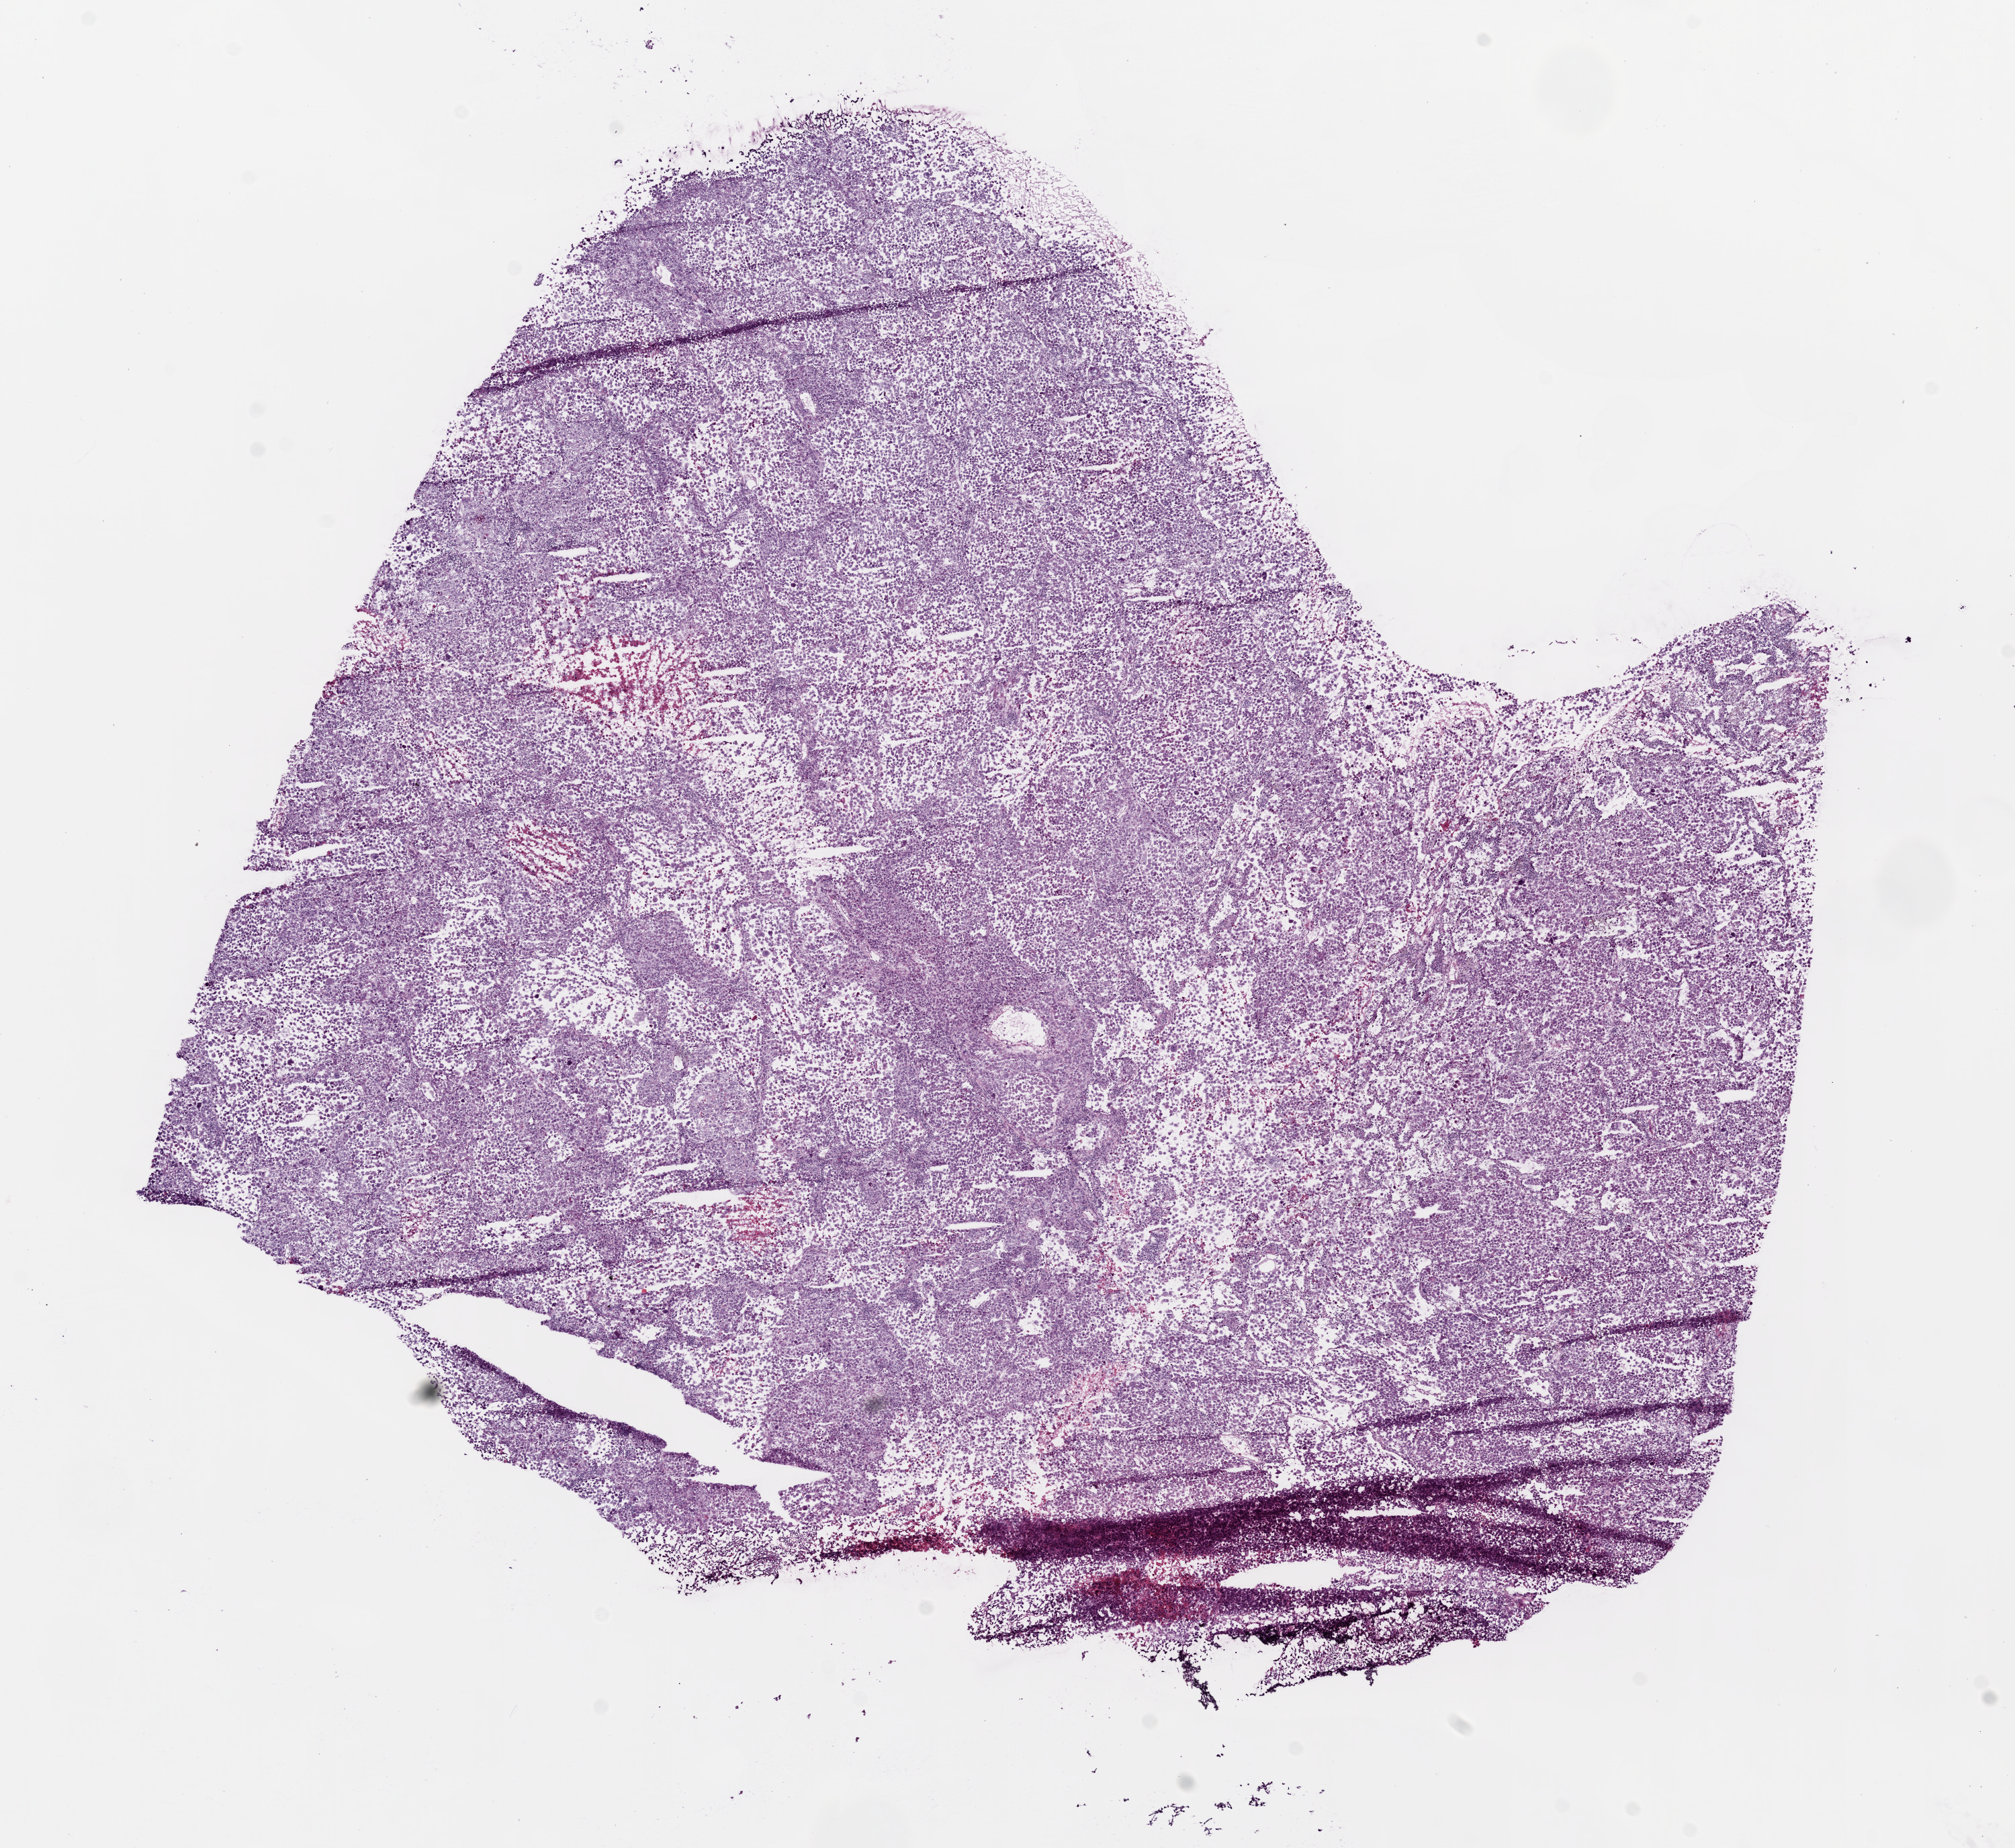
Hematoxylin and eosin (H&E) stained whole-slide image, shown as a low-resolution overview of the whole scanned area (about 12.0 x 11.0 mm); frozen section; primary tumour sample from the lung. Patient: male, age at initial diagnosis 57 years. Composition of this section per pathologist review: tumour cells 90%, tumour nuclei 80%, normal cells 0%, stromal cells 5%, necrosis 10%.
AJCC pathologic stage: IIIB (6th edition). Laterality: left. Diagnosis: Adenocarcinoma with mixed subtypes (lower lobe, lung). TNM: T4 N2 M0.